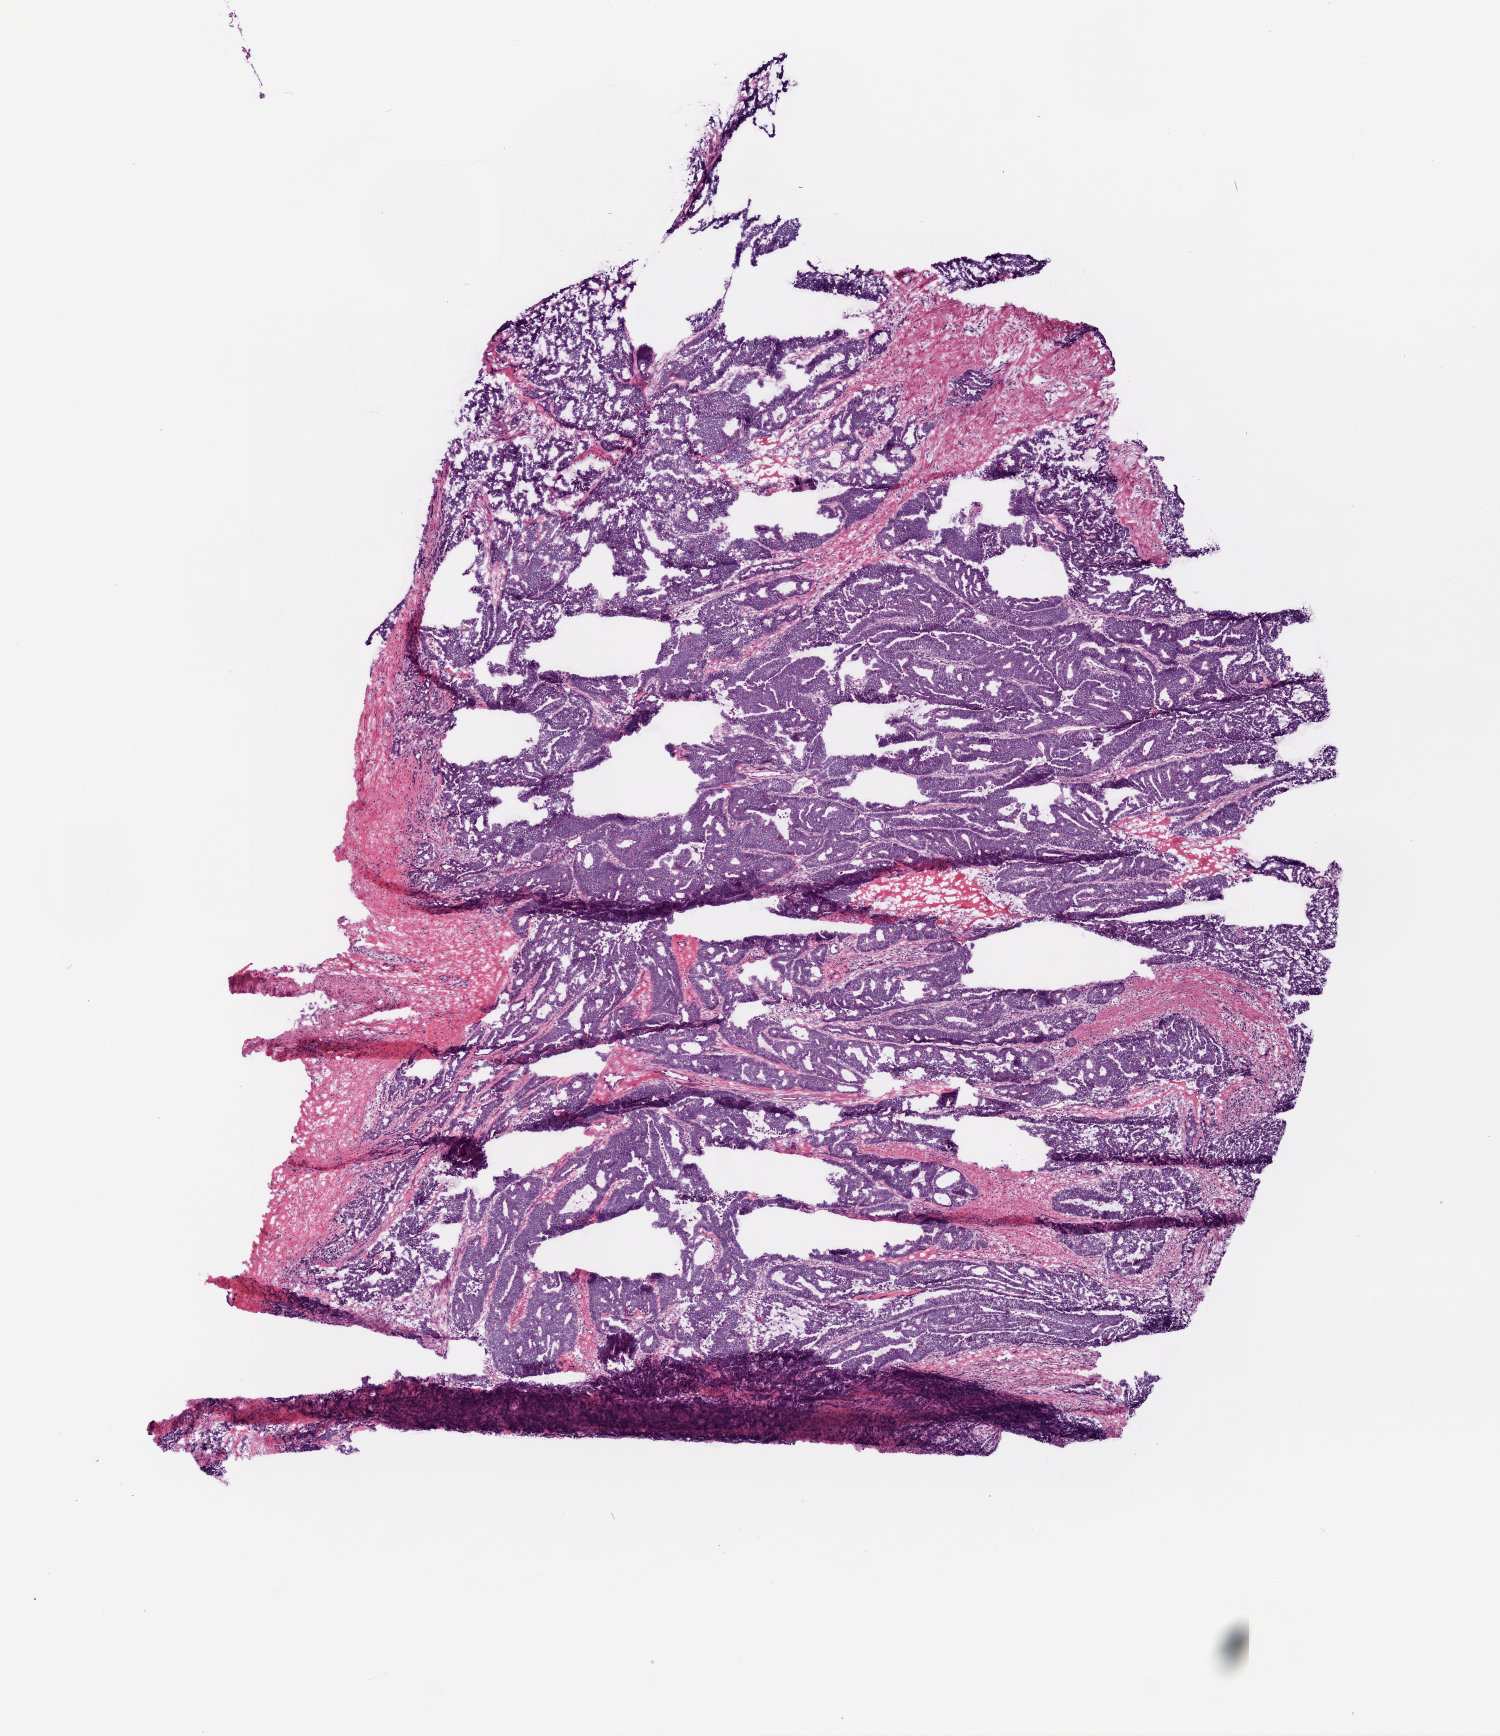
H&E-stained whole-slide image, shown as a low-resolution overview of the whole scanned area (about 6.0 x 7.0 mm), frozen section, sample: primary tumour, colon. Male, age 69 years at initial diagnosis. Slide review estimates, as recorded: tumour cells 80%, tumour nuclei 90%, normal cells 0%, stromal cells 10%, necrosis 10%.
TNM: T4 N1 M1. Diagnosis: Adenocarcinoma, NOS. AJCC pathologic stage: IV (5th edition).